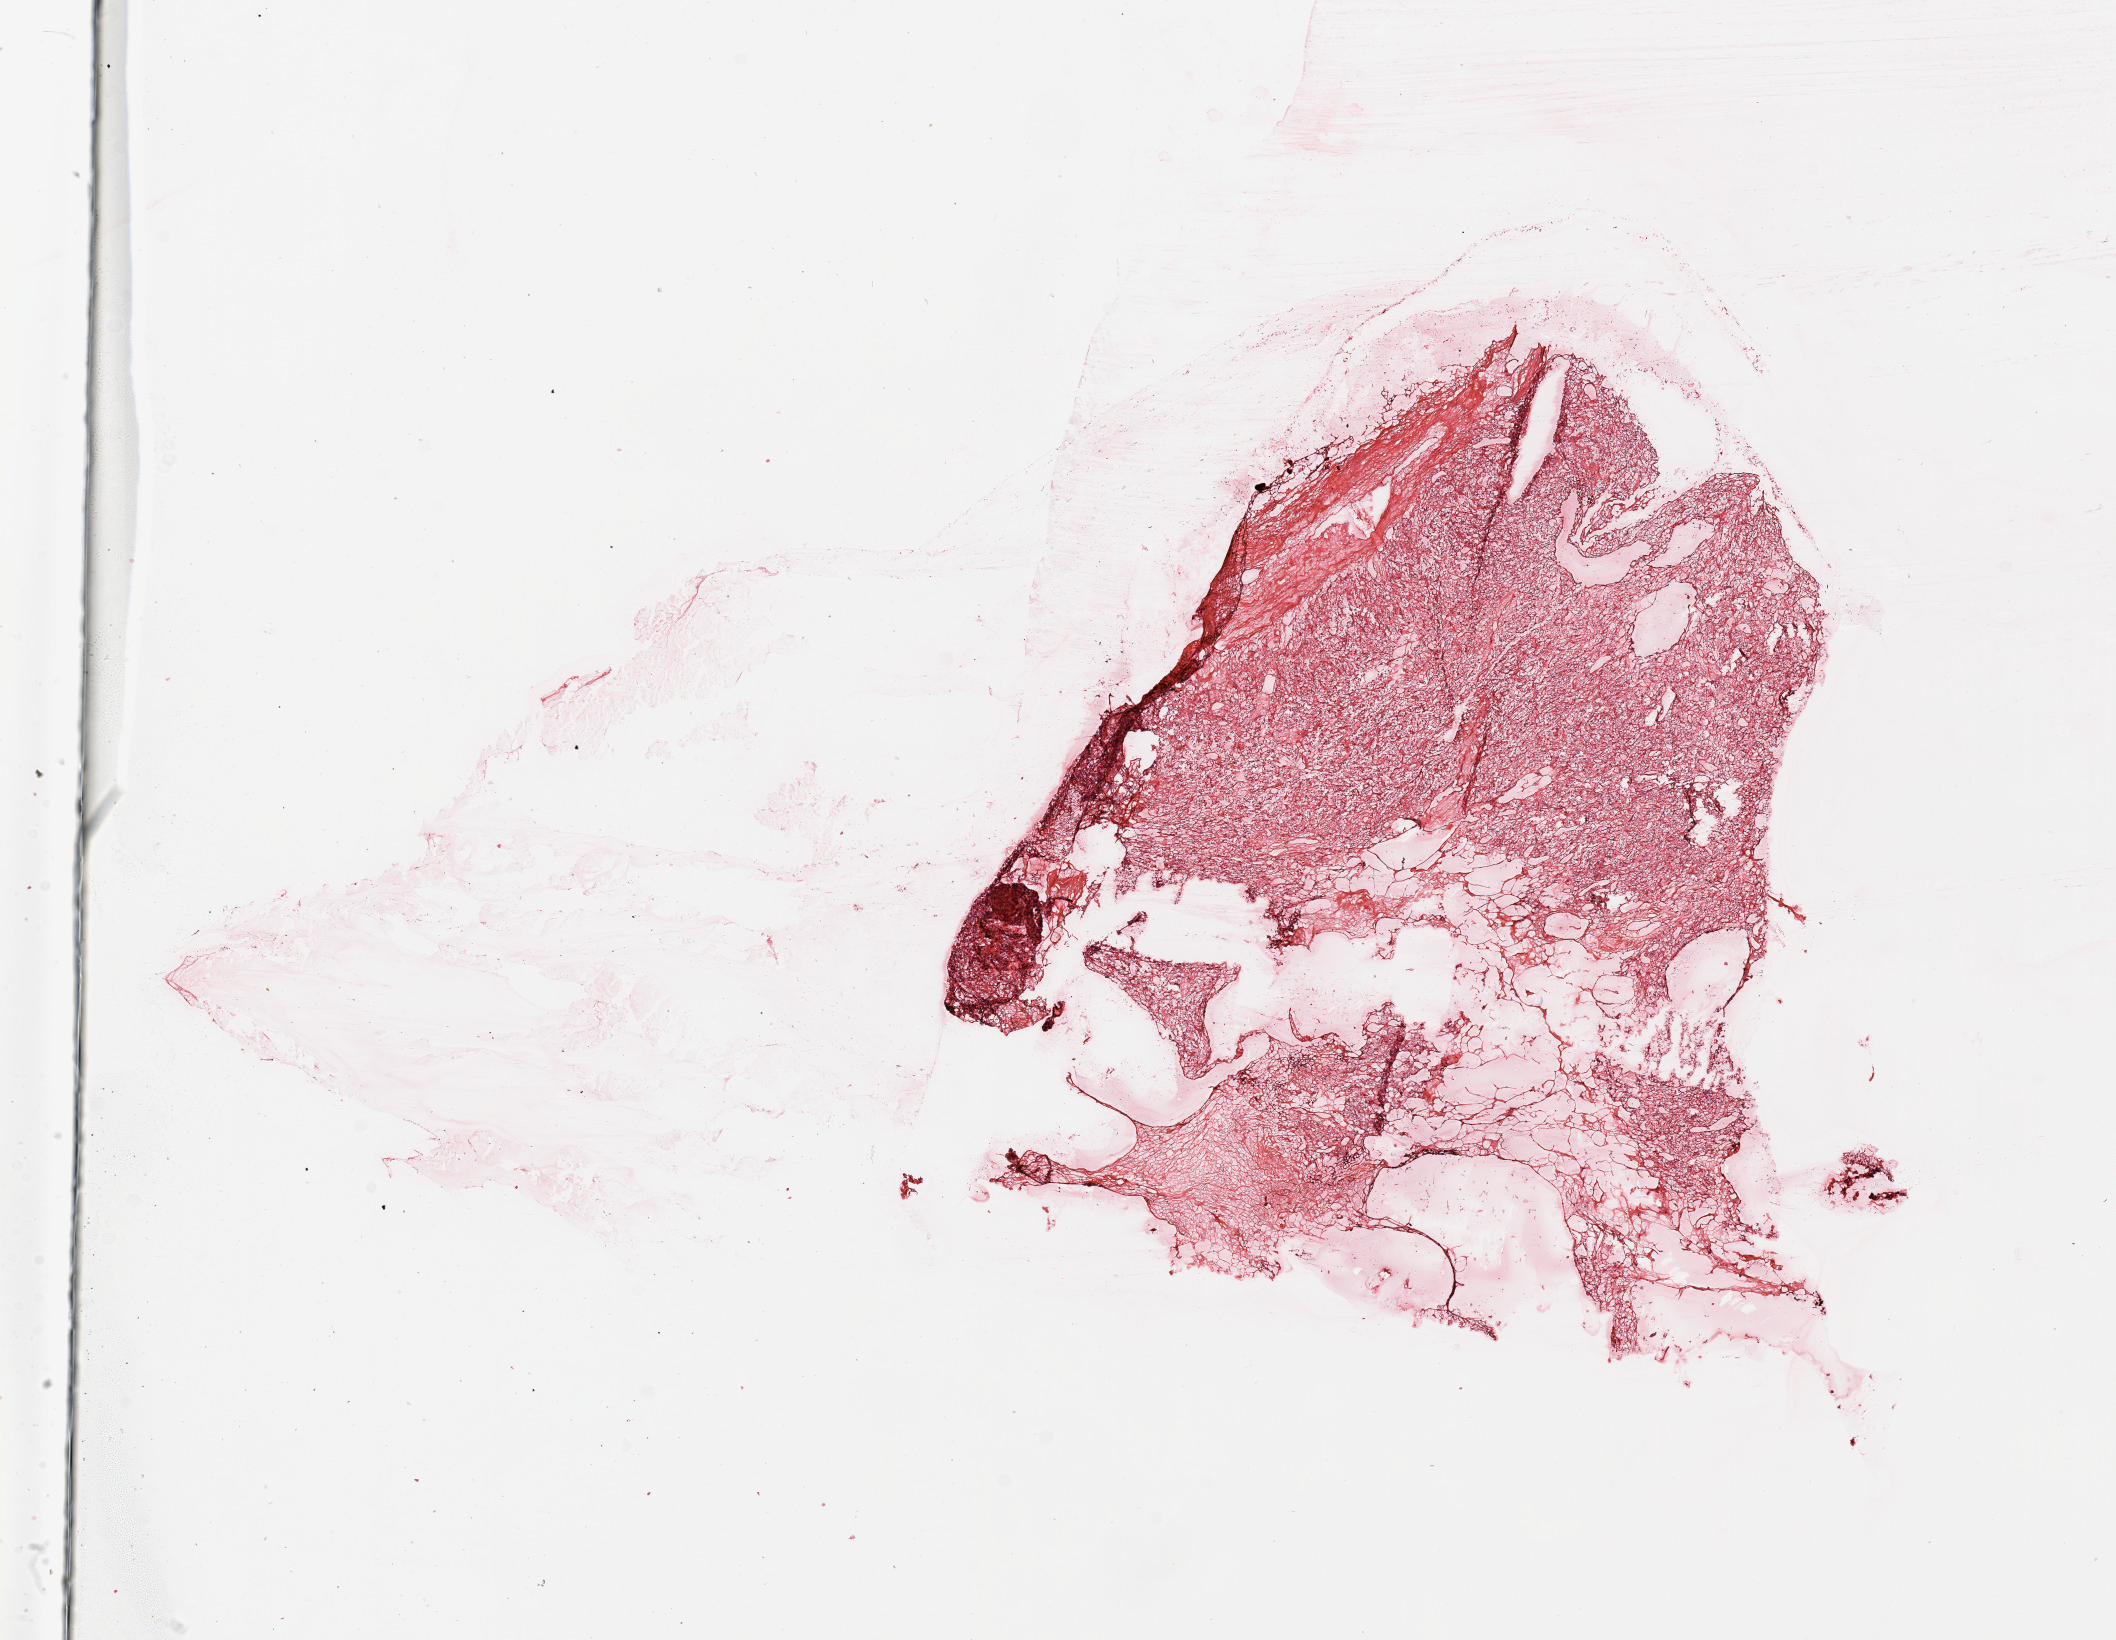
Whole-slide histology image, Hematoxylin and eosin (H&E) stained — a low-resolution overview of the entire scanned area, about 16.7 x 13.0 mm, tumour tissue sample, sampled site: kidney. Male, 58 y/o. Histologic grade: G2 (moderately differentiated). Slide review estimates, as recorded: tumour nuclei 80%, necrosis 30%.
* primary tumour site (as recorded): upper pole
* diagnosis: Renal cell carcinoma, NOS
* AJCC pathologic stage: IV